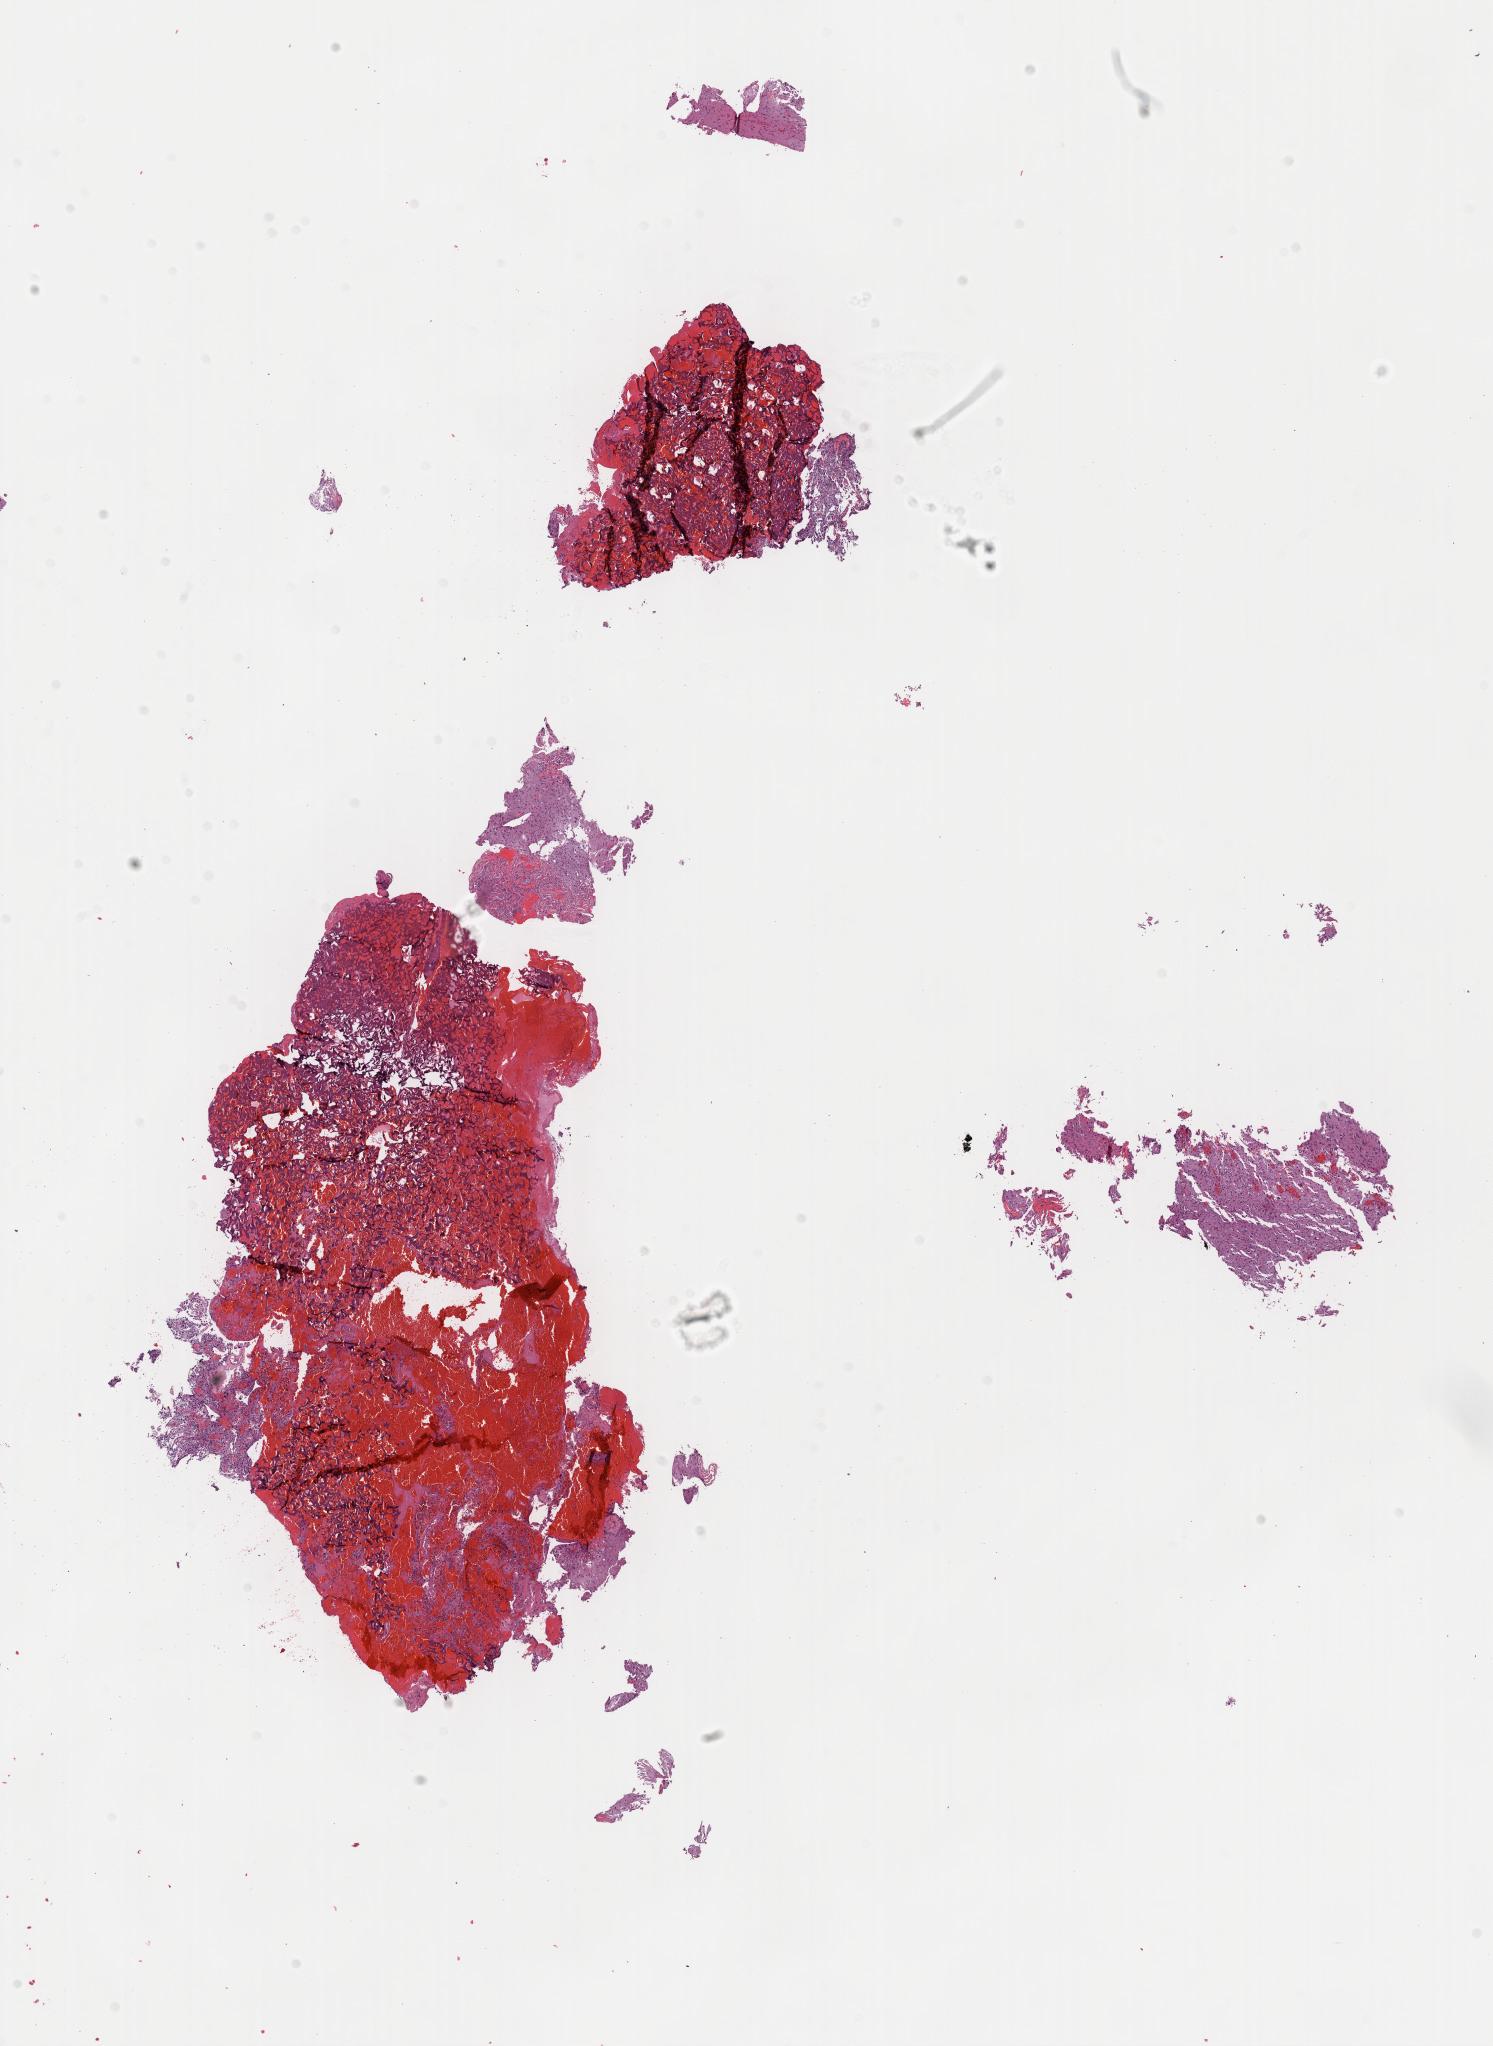
Hematoxylin and eosin (H&E) stained whole-slide image — whole scanned area (about 12.1 x 16.6 mm) shown as a low-resolution overview, formalin-fixed paraffin-embedded (FFPE) diagnostic section, brain, primary tumour sample. Male, age 26 years at initial diagnosis. Histologic grade: G2 (moderately differentiated).
Pathologic diagnosis: Astrocytoma, NOS.